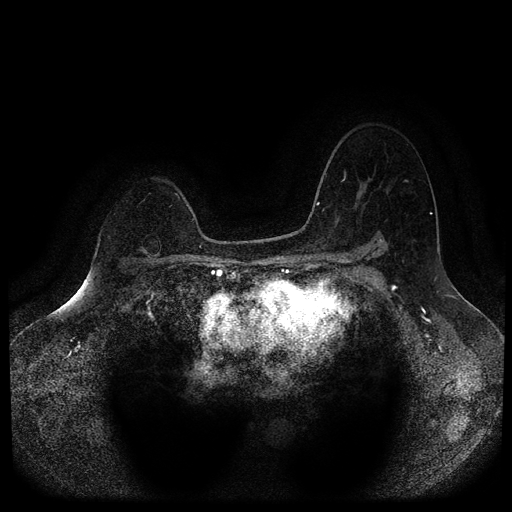
Breast MRI (dynamic contrast-enhanced, multi-phase), one axial slice. Position 75 of 116 along the scan axis. Dynamic contrast-enhanced series, time point 2 of 5 at this slice position (early post-contrast). 1.5 T. TE 2.6 ms, TR 5.4 ms. 512 × 512 image matrix. Female patient, age 64 years.
Outlined on this slice (semi-automatically segmented with operator editing):
- breast lesion (labelled benign in the annotation): bounding box [x1, y1, x2, y2] px = [140, 233, 161, 257]